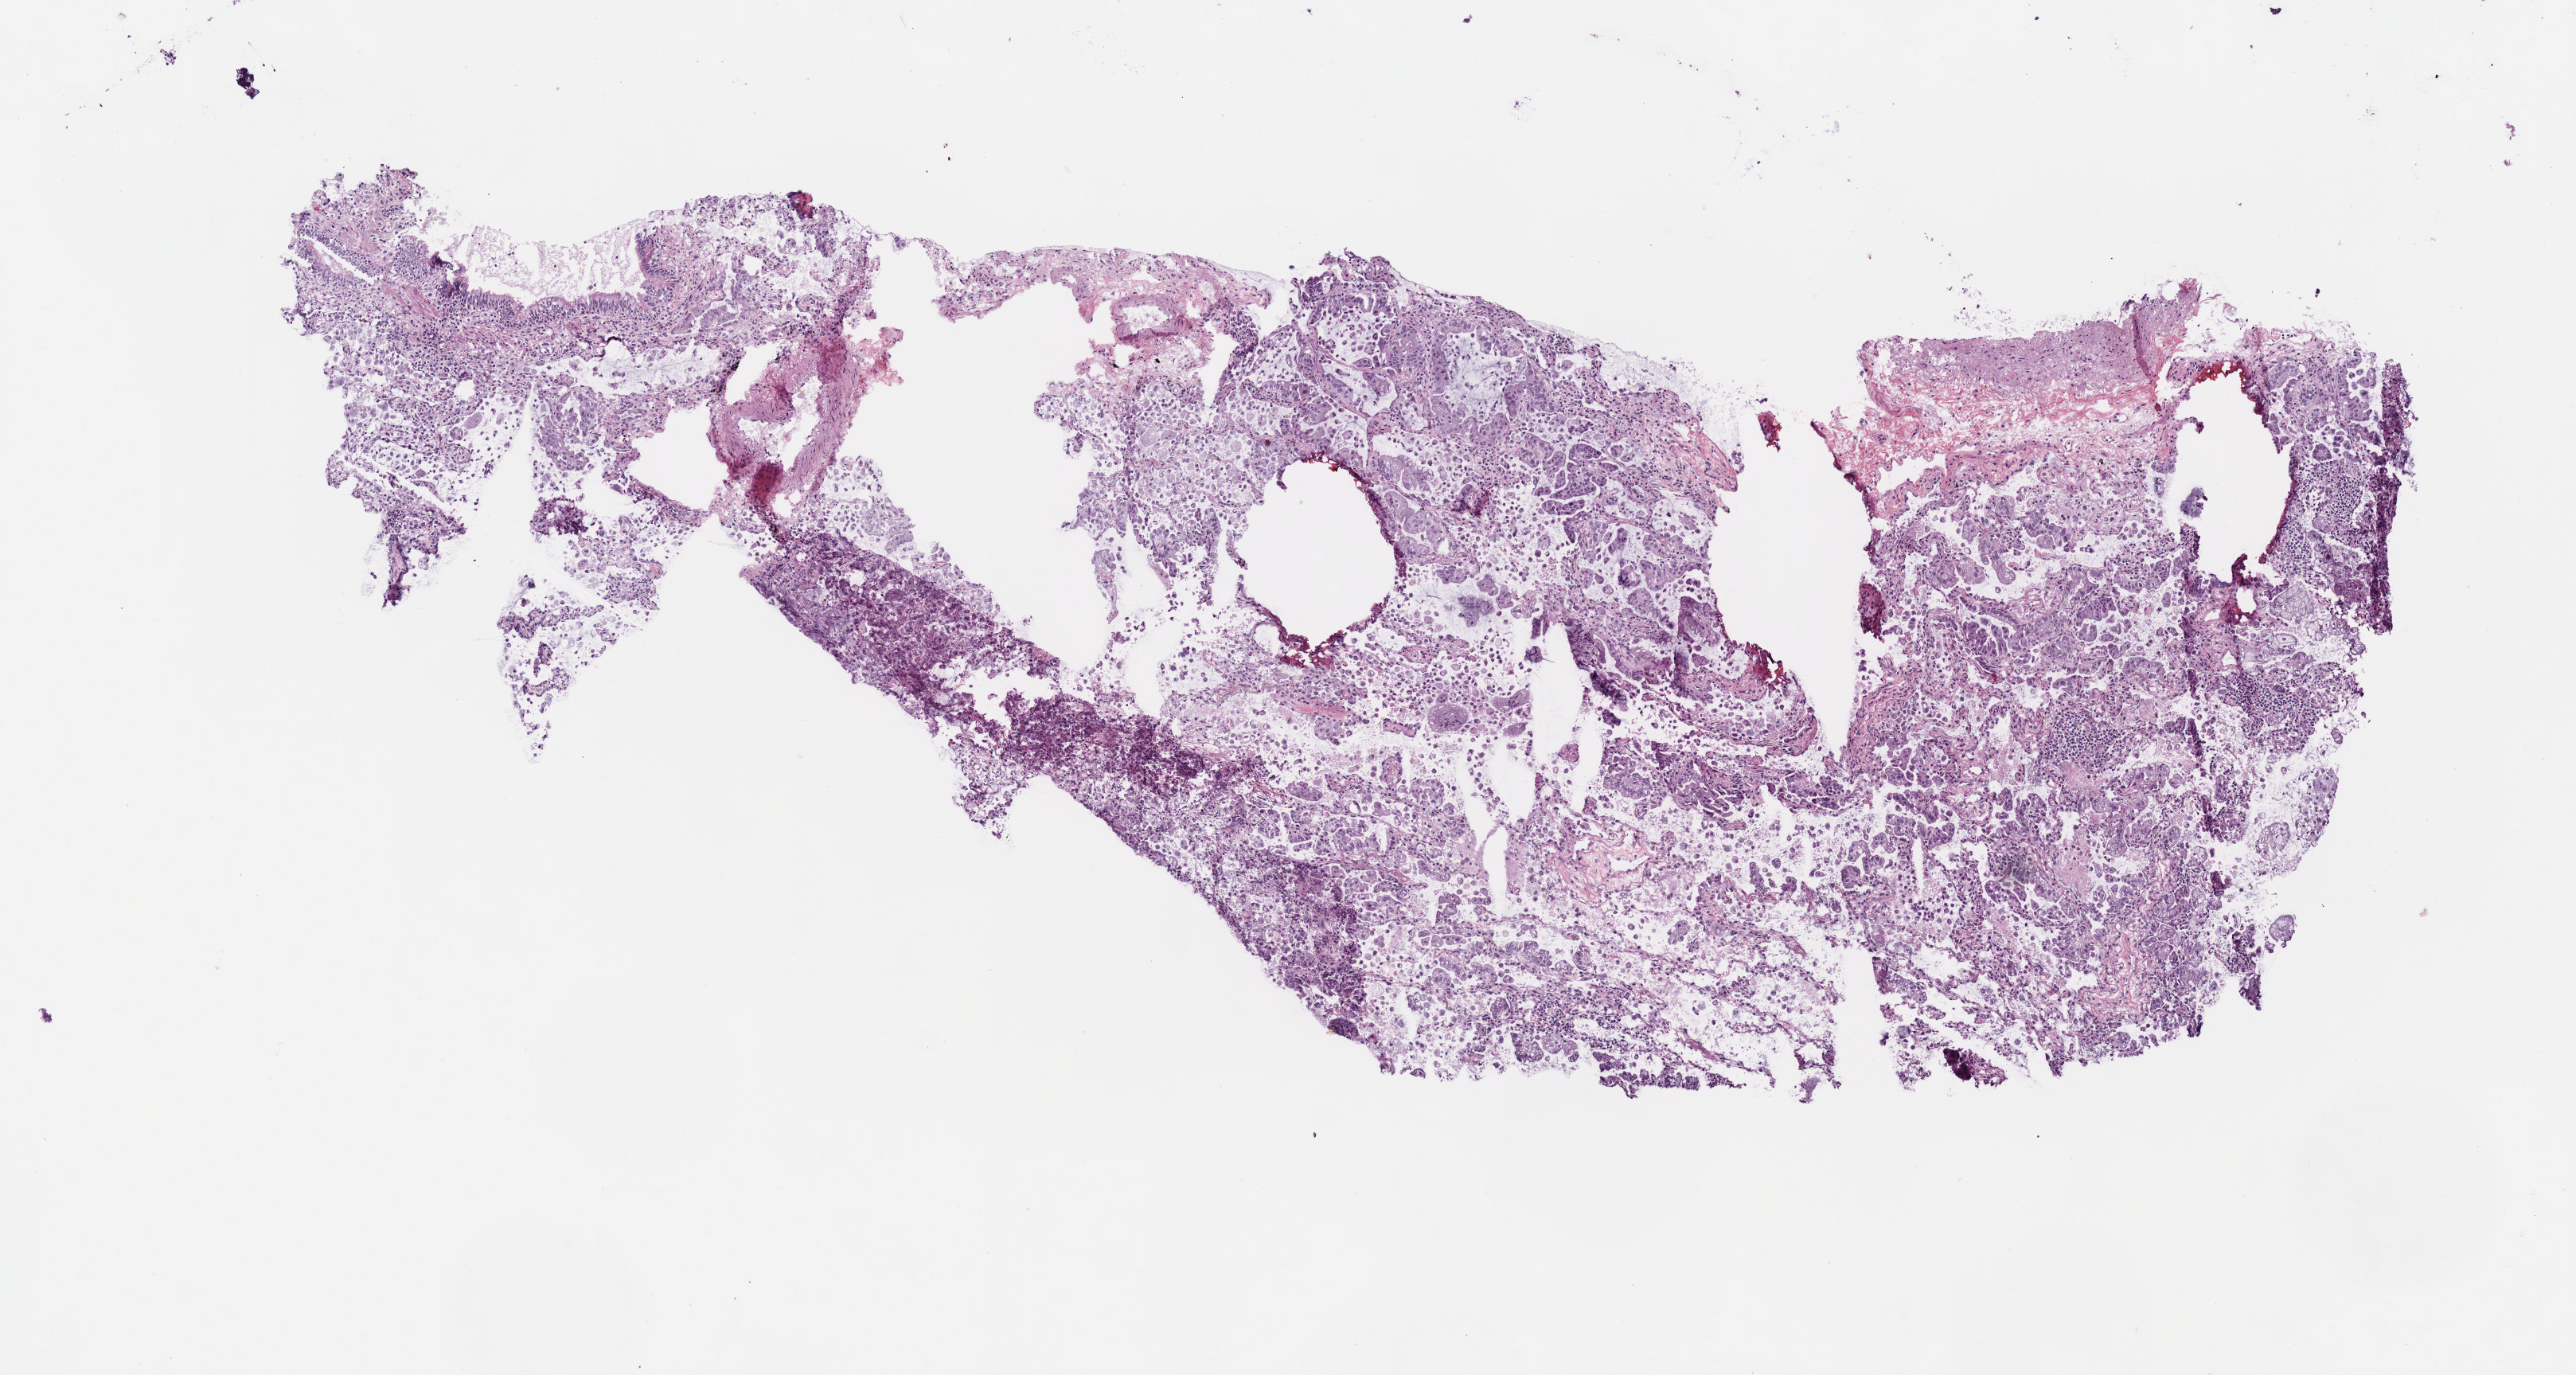
Digitized H&E-stained tissue section (whole slide) — whole scanned area (about 6.5 x 3.5 mm, acquisition: 40x scan) shown as a low-resolution overview. Frozen section from the top of the tissue portion. Sample: primary tumour, lung. Patient: male, age at initial diagnosis 77 years. Slide review estimates, as recorded: tumour cells 89%, tumour nuclei 70%, normal cells 2%, stromal cells 9%, necrosis 0%. Infiltration values recorded for this section: lymphocyte infiltration 10%, monocyte infiltration 20%, neutrophil infiltration 0%.
Histologic diagnosis: Mucinous adenocarcinoma (lower lobe, lung). AJCC pathologic stage: IIB (7th edition). TNM: T3 N0 MX. Laterality: right.